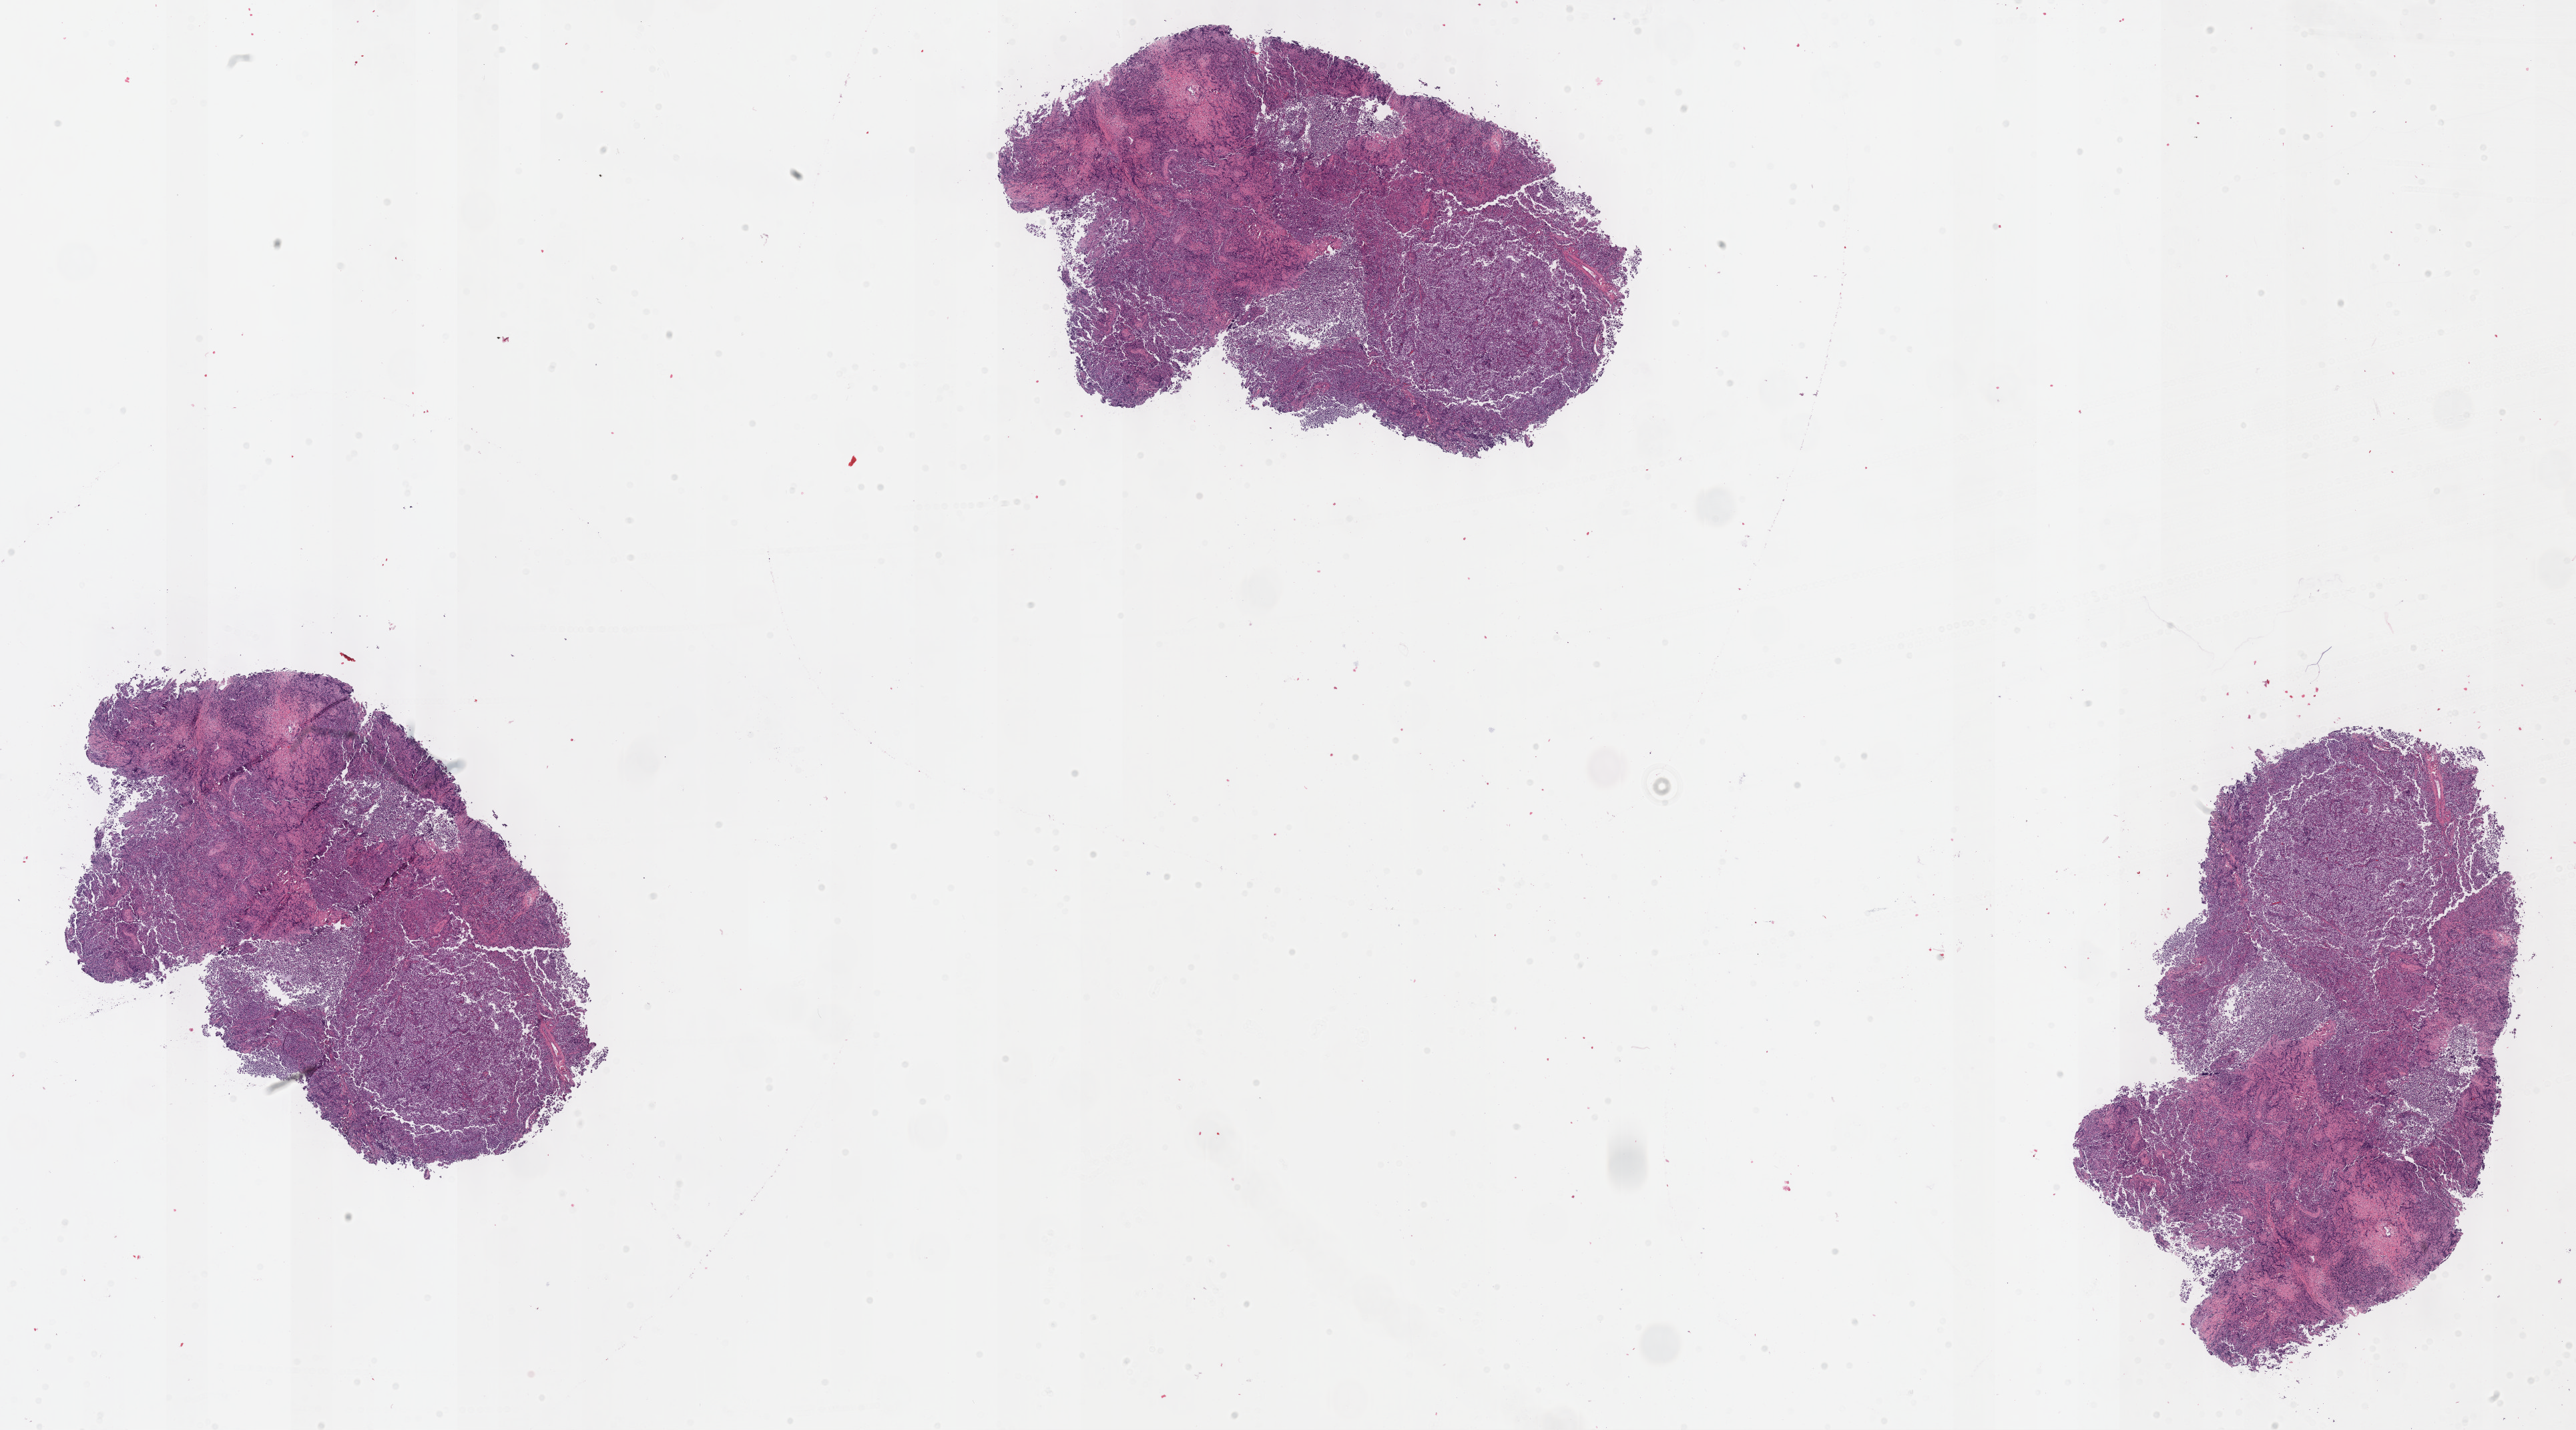
Hematoxylin and eosin (H&E) stained whole-slide image, shown as a low-resolution overview of the whole scanned area (about 31.2 x 17.3 mm, slide scanned at 40x), formalin-fixed paraffin-embedded (FFPE) diagnostic section, testis, primary tumour sample. Male, age 42 years at initial diagnosis.
Histologic diagnosis: Seminoma, NOS. Laterality: left. AJCC pathologic stage: I.